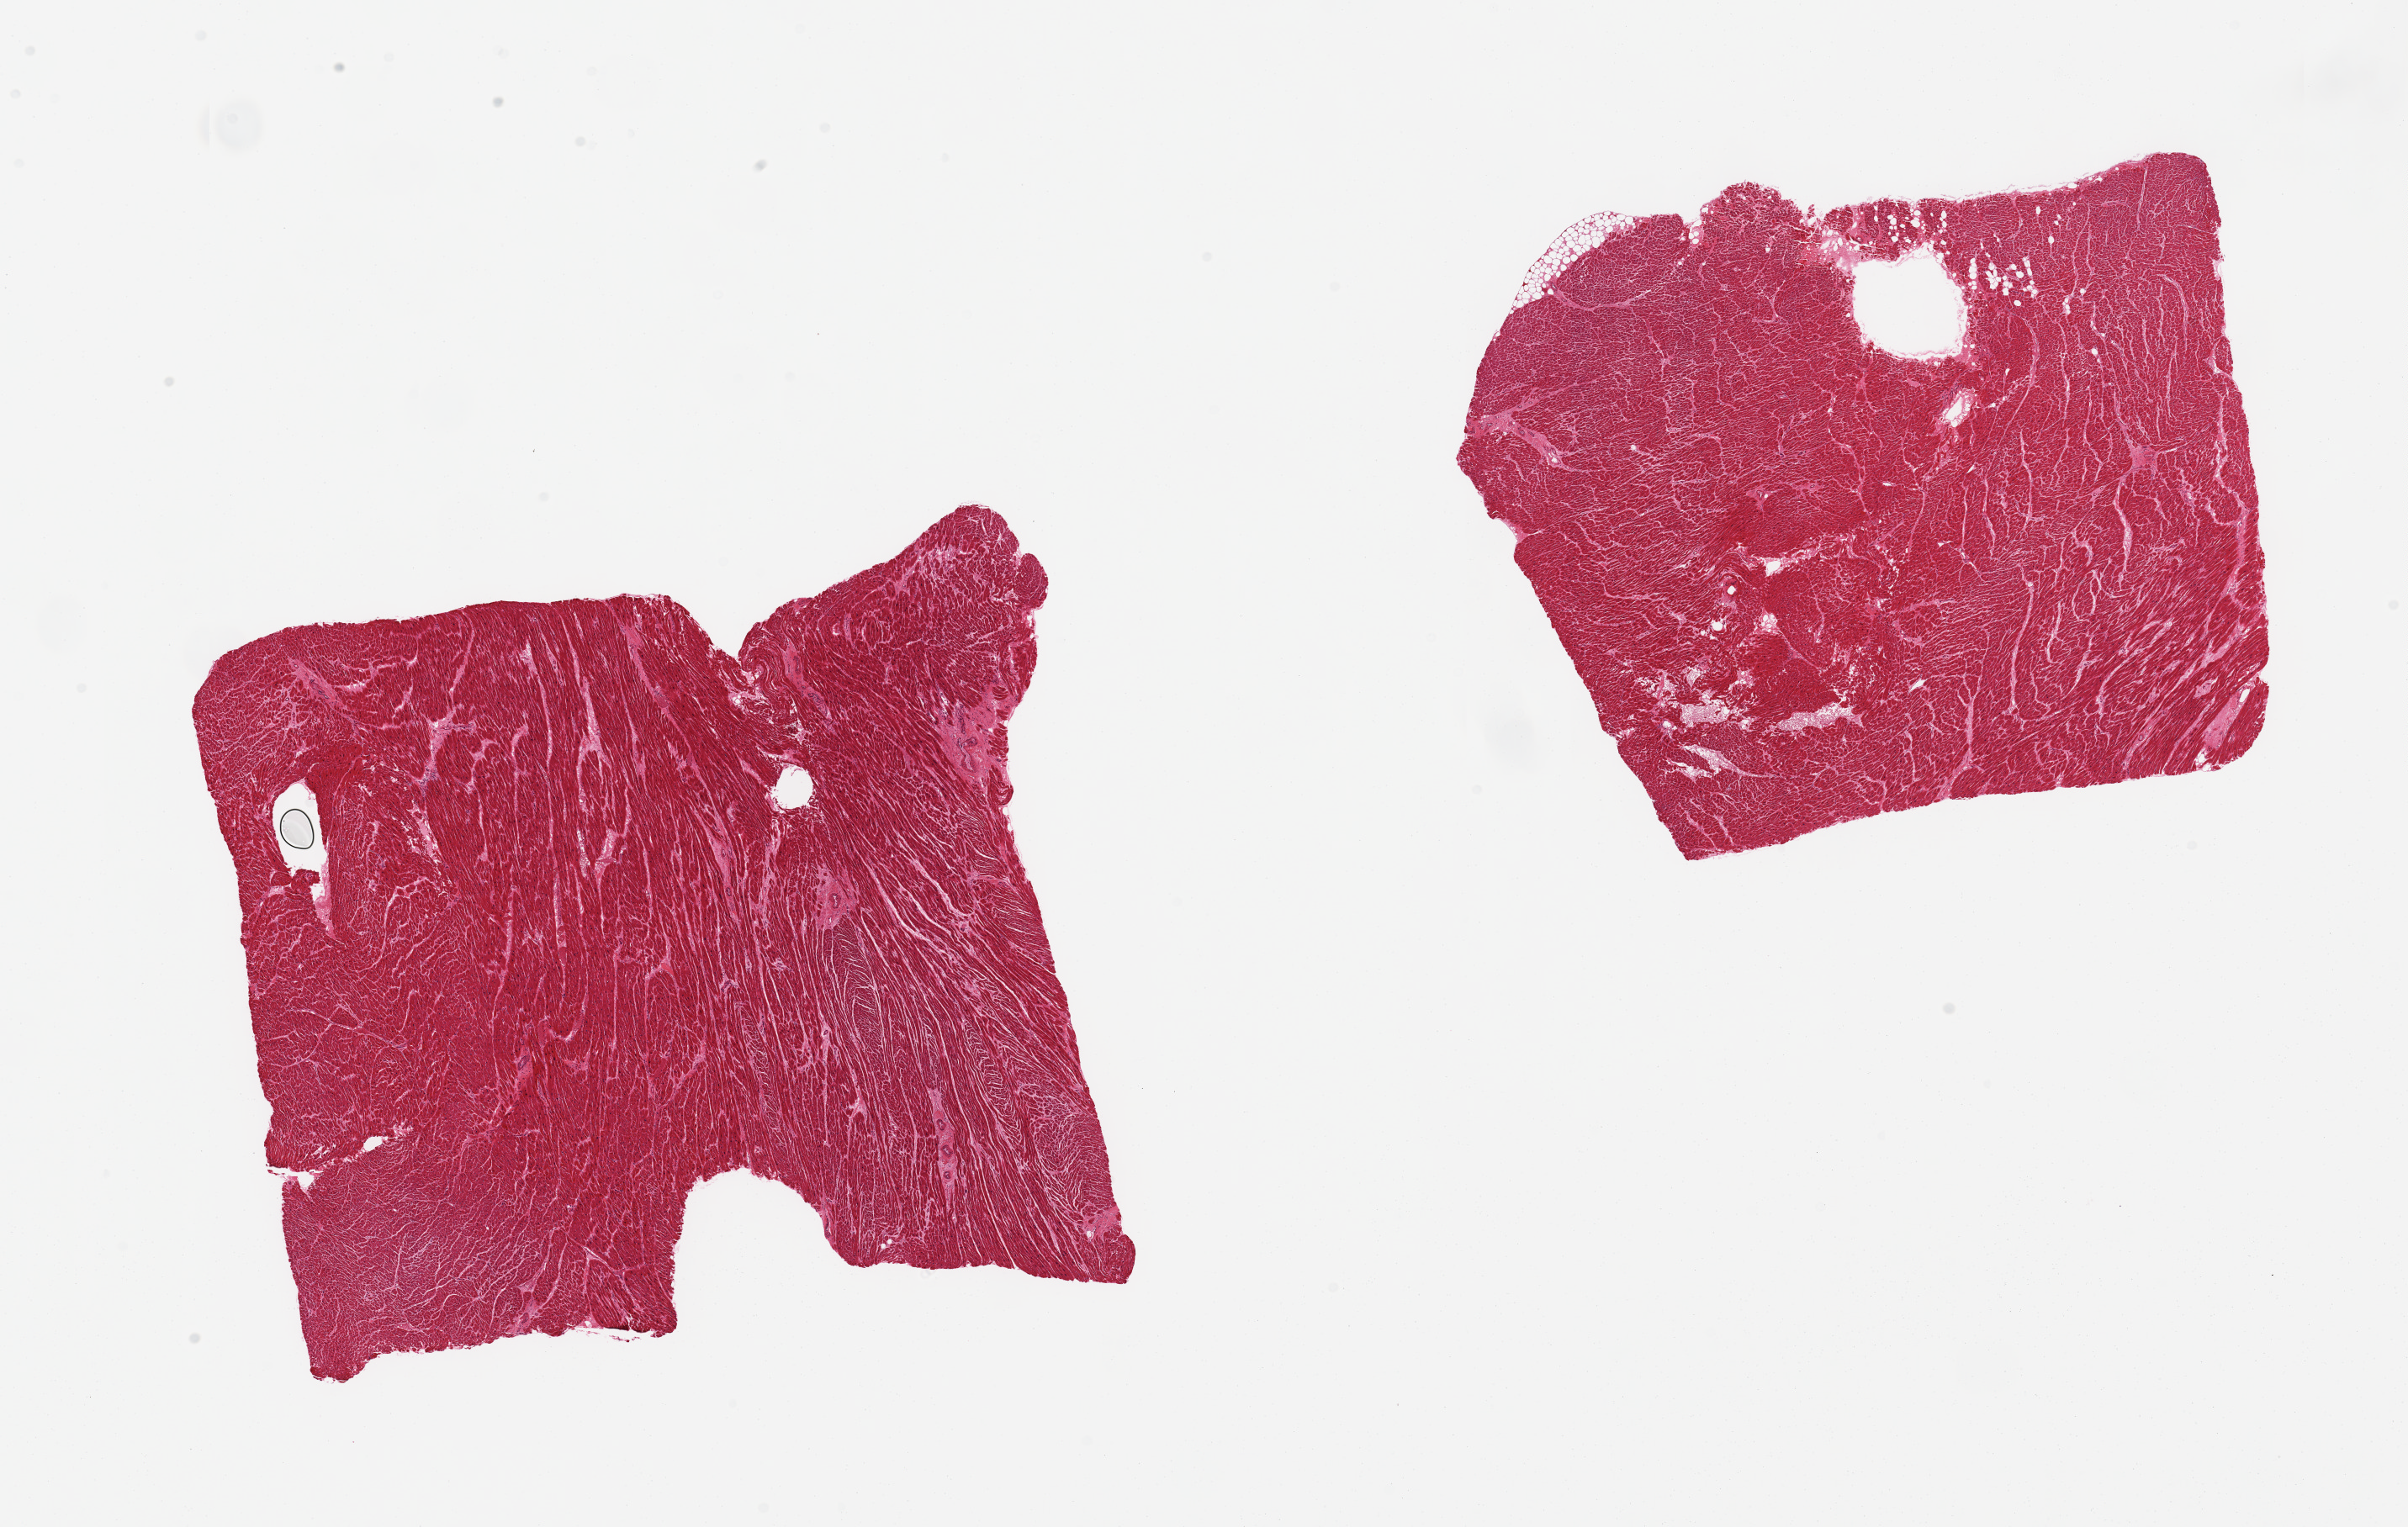
H&E whole-slide image, brightfield, low-resolution overview of the scanned area, about 22.6 x 14.4 mm, PAXgene-fixed paraffin-embedded (PFPE) section, section of heart (target tissue), donor tissue sample.
Review note (as recorded): 2 pieces, minimal-mild interstitital fibrosis; occasional contraction band noted.